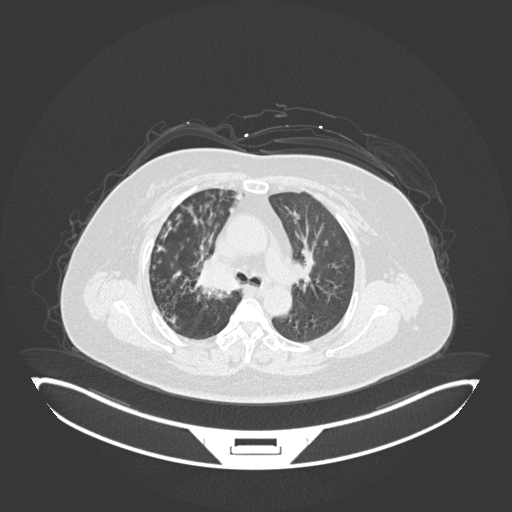
Chest CT, one axial slice; slice 117 of 245 in the series (ordered by position); reconstruction kernel B30f; lung window (W 1500 / L -600 HU); 1 mm slice thickness; 512 × 512 image matrix. Female patient, age 60 years. From the clinical record (not read from this slice): clinical TNM (as recorded): T1c N0 M0; histopathological grade: G1-G2.
Annotated regions visible in this slice (bounding box drawn by a radiologist):
- lung tumour (recorded histology: squamous cell carcinoma): bounding box (x1, y1, x2, y2) in pixels: (193, 253, 246, 295)